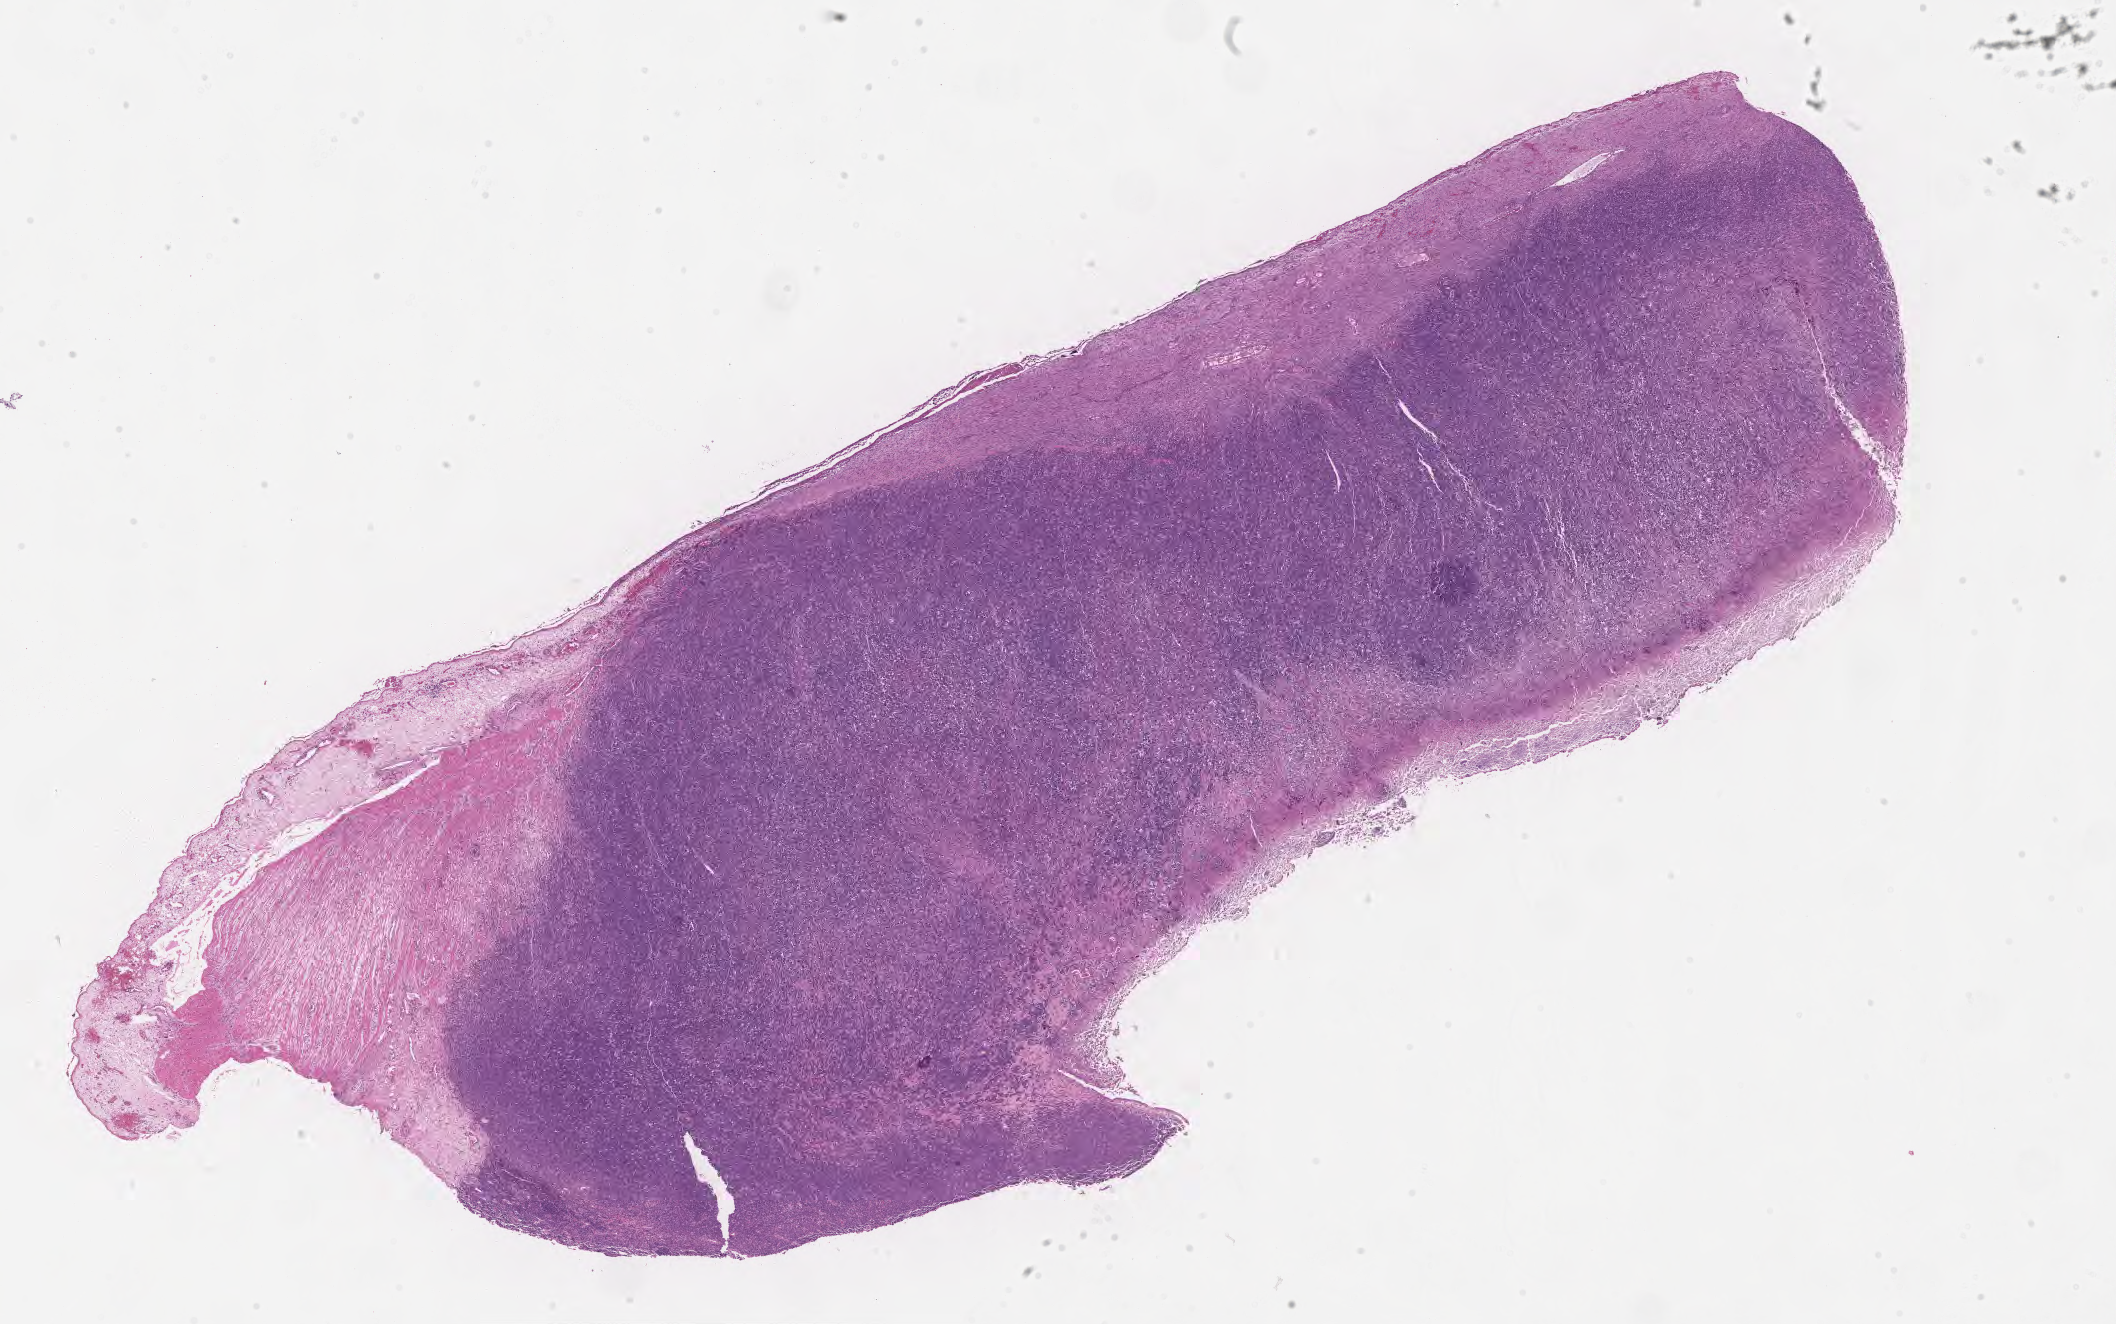
H&E whole-slide image — a low-resolution overview of the entire scanned area, about 17.1 x 10.7 mm, tumor tissue, anatomic site: small intestine. Male patient; age at initial diagnosis 3 years.
Histologic diagnosis: Burkitt lymphoma, NOS.